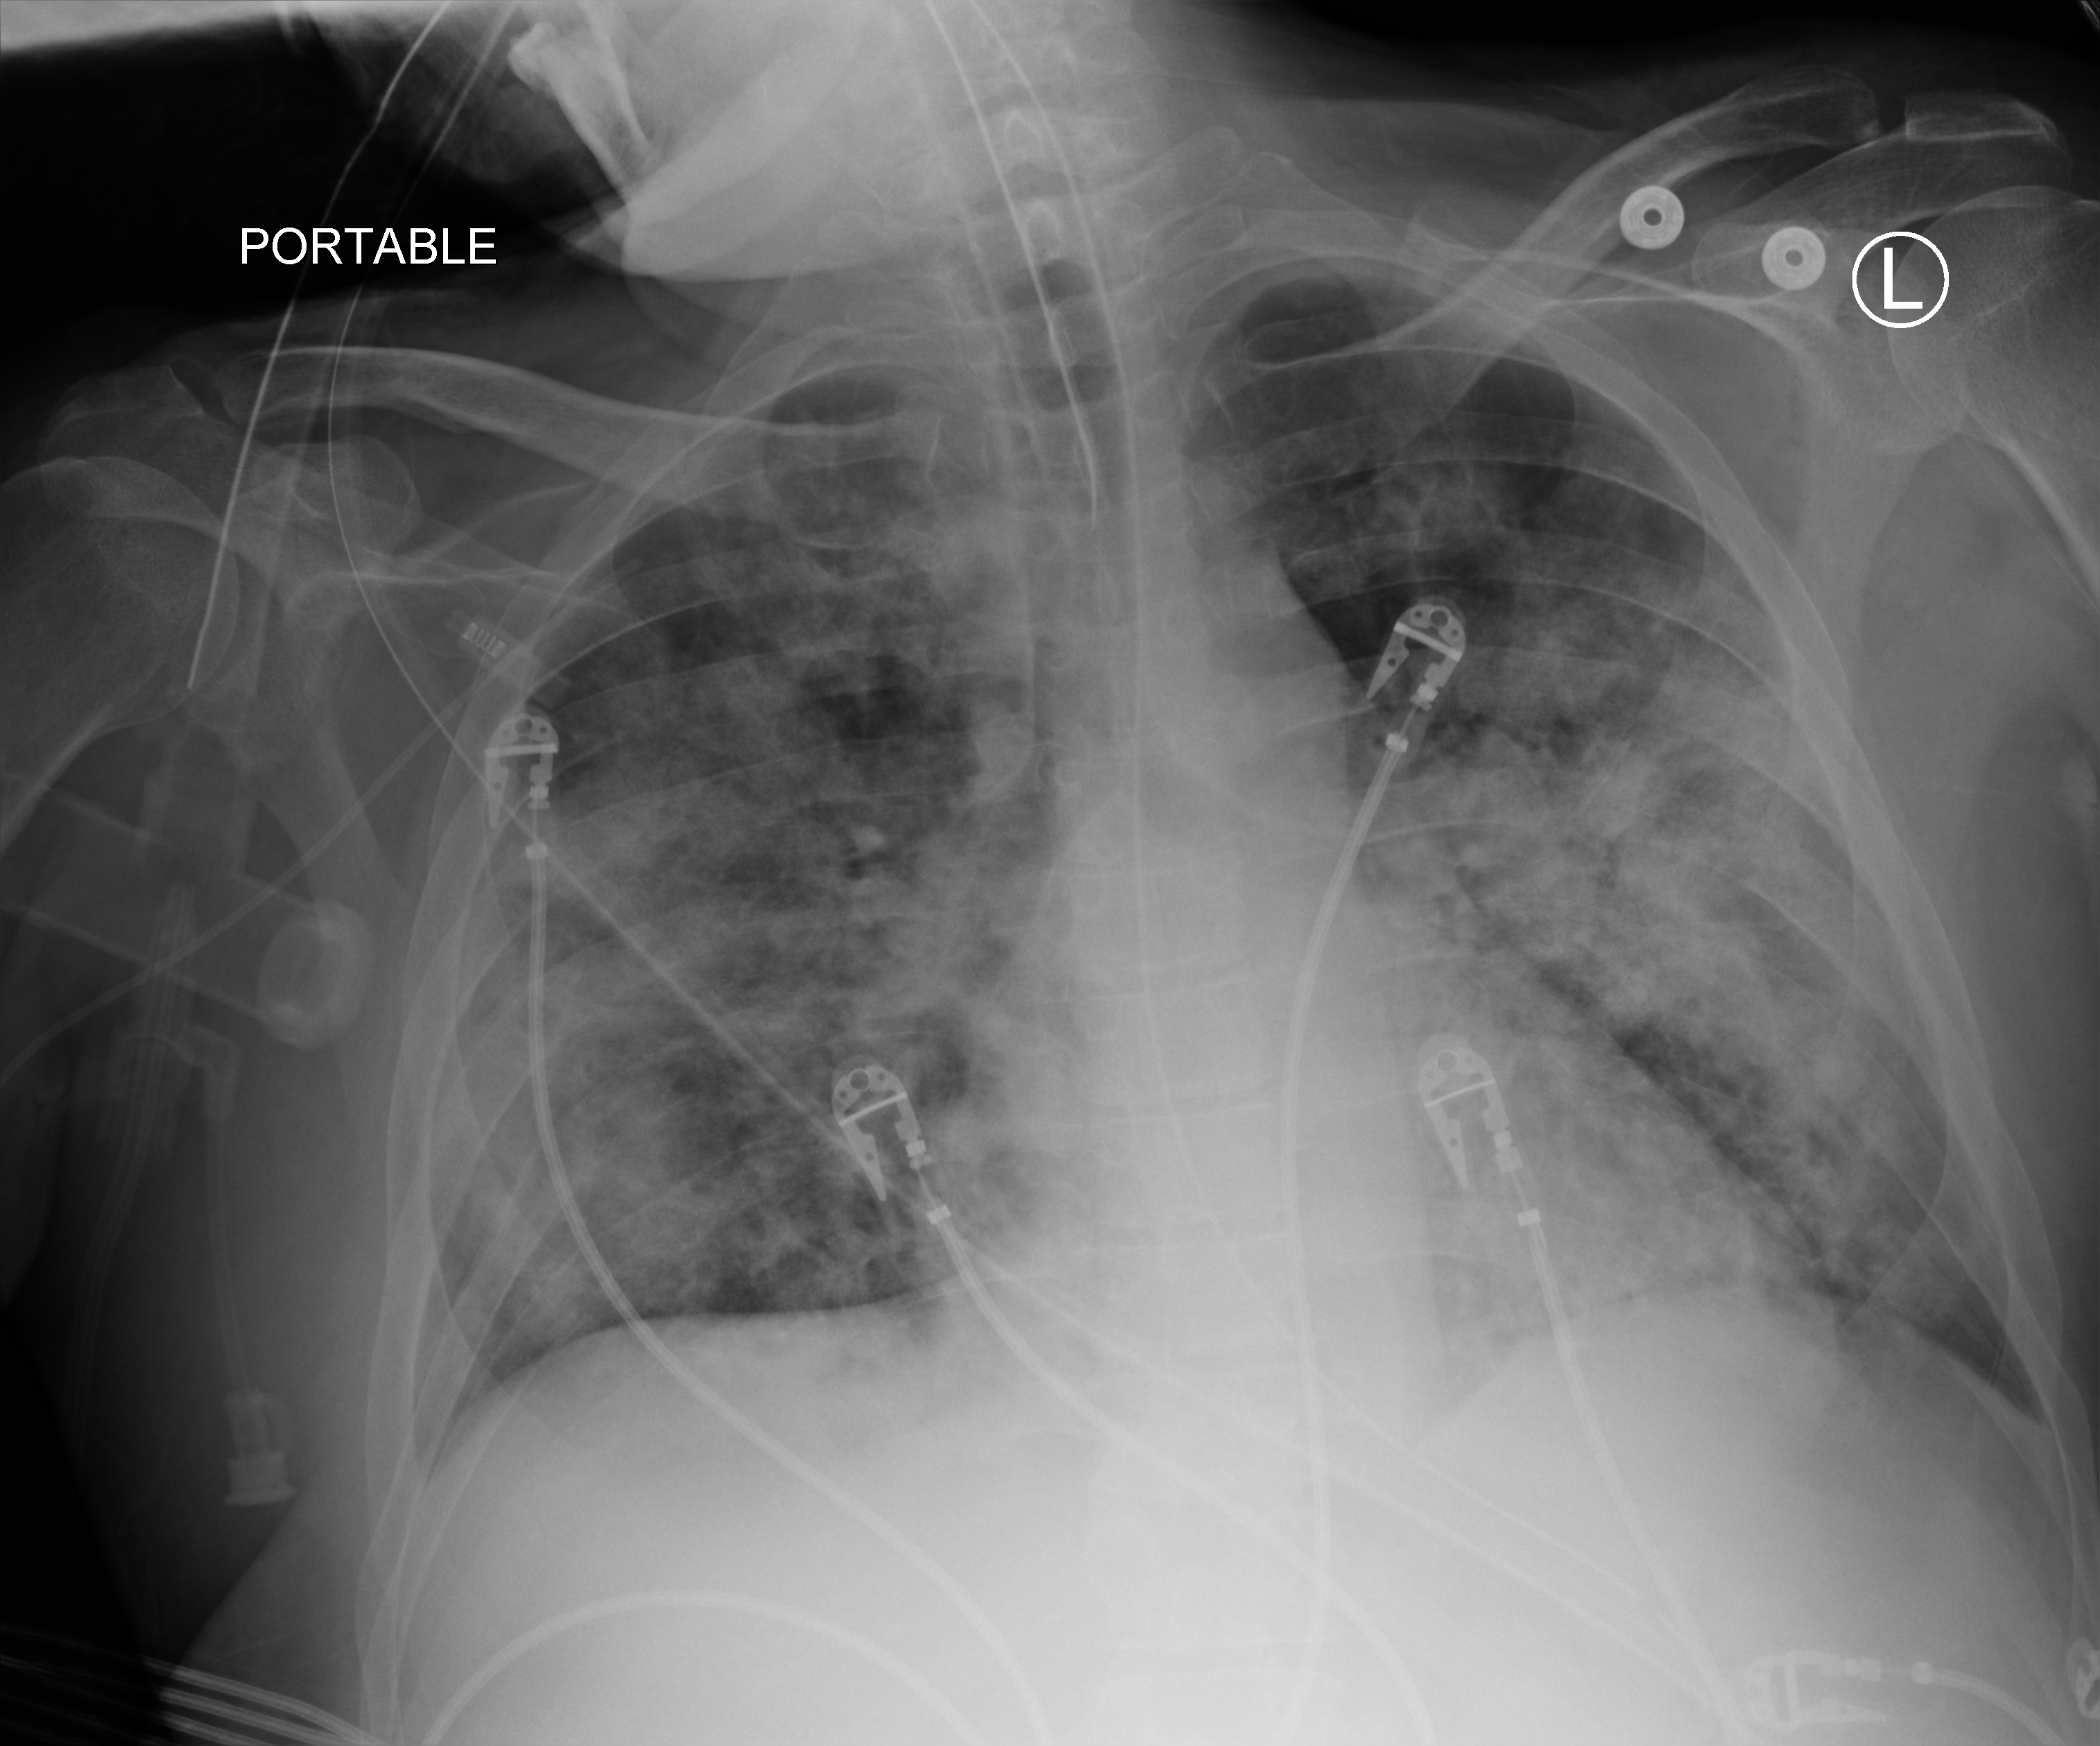
Chest X-ray (portable). Patient hospitalised with COVID-19; male, aged 18–59 years.
Admission-level facts for this patient (not findings on this image; timing relative to this image not recorded): COPD (admission record): no.